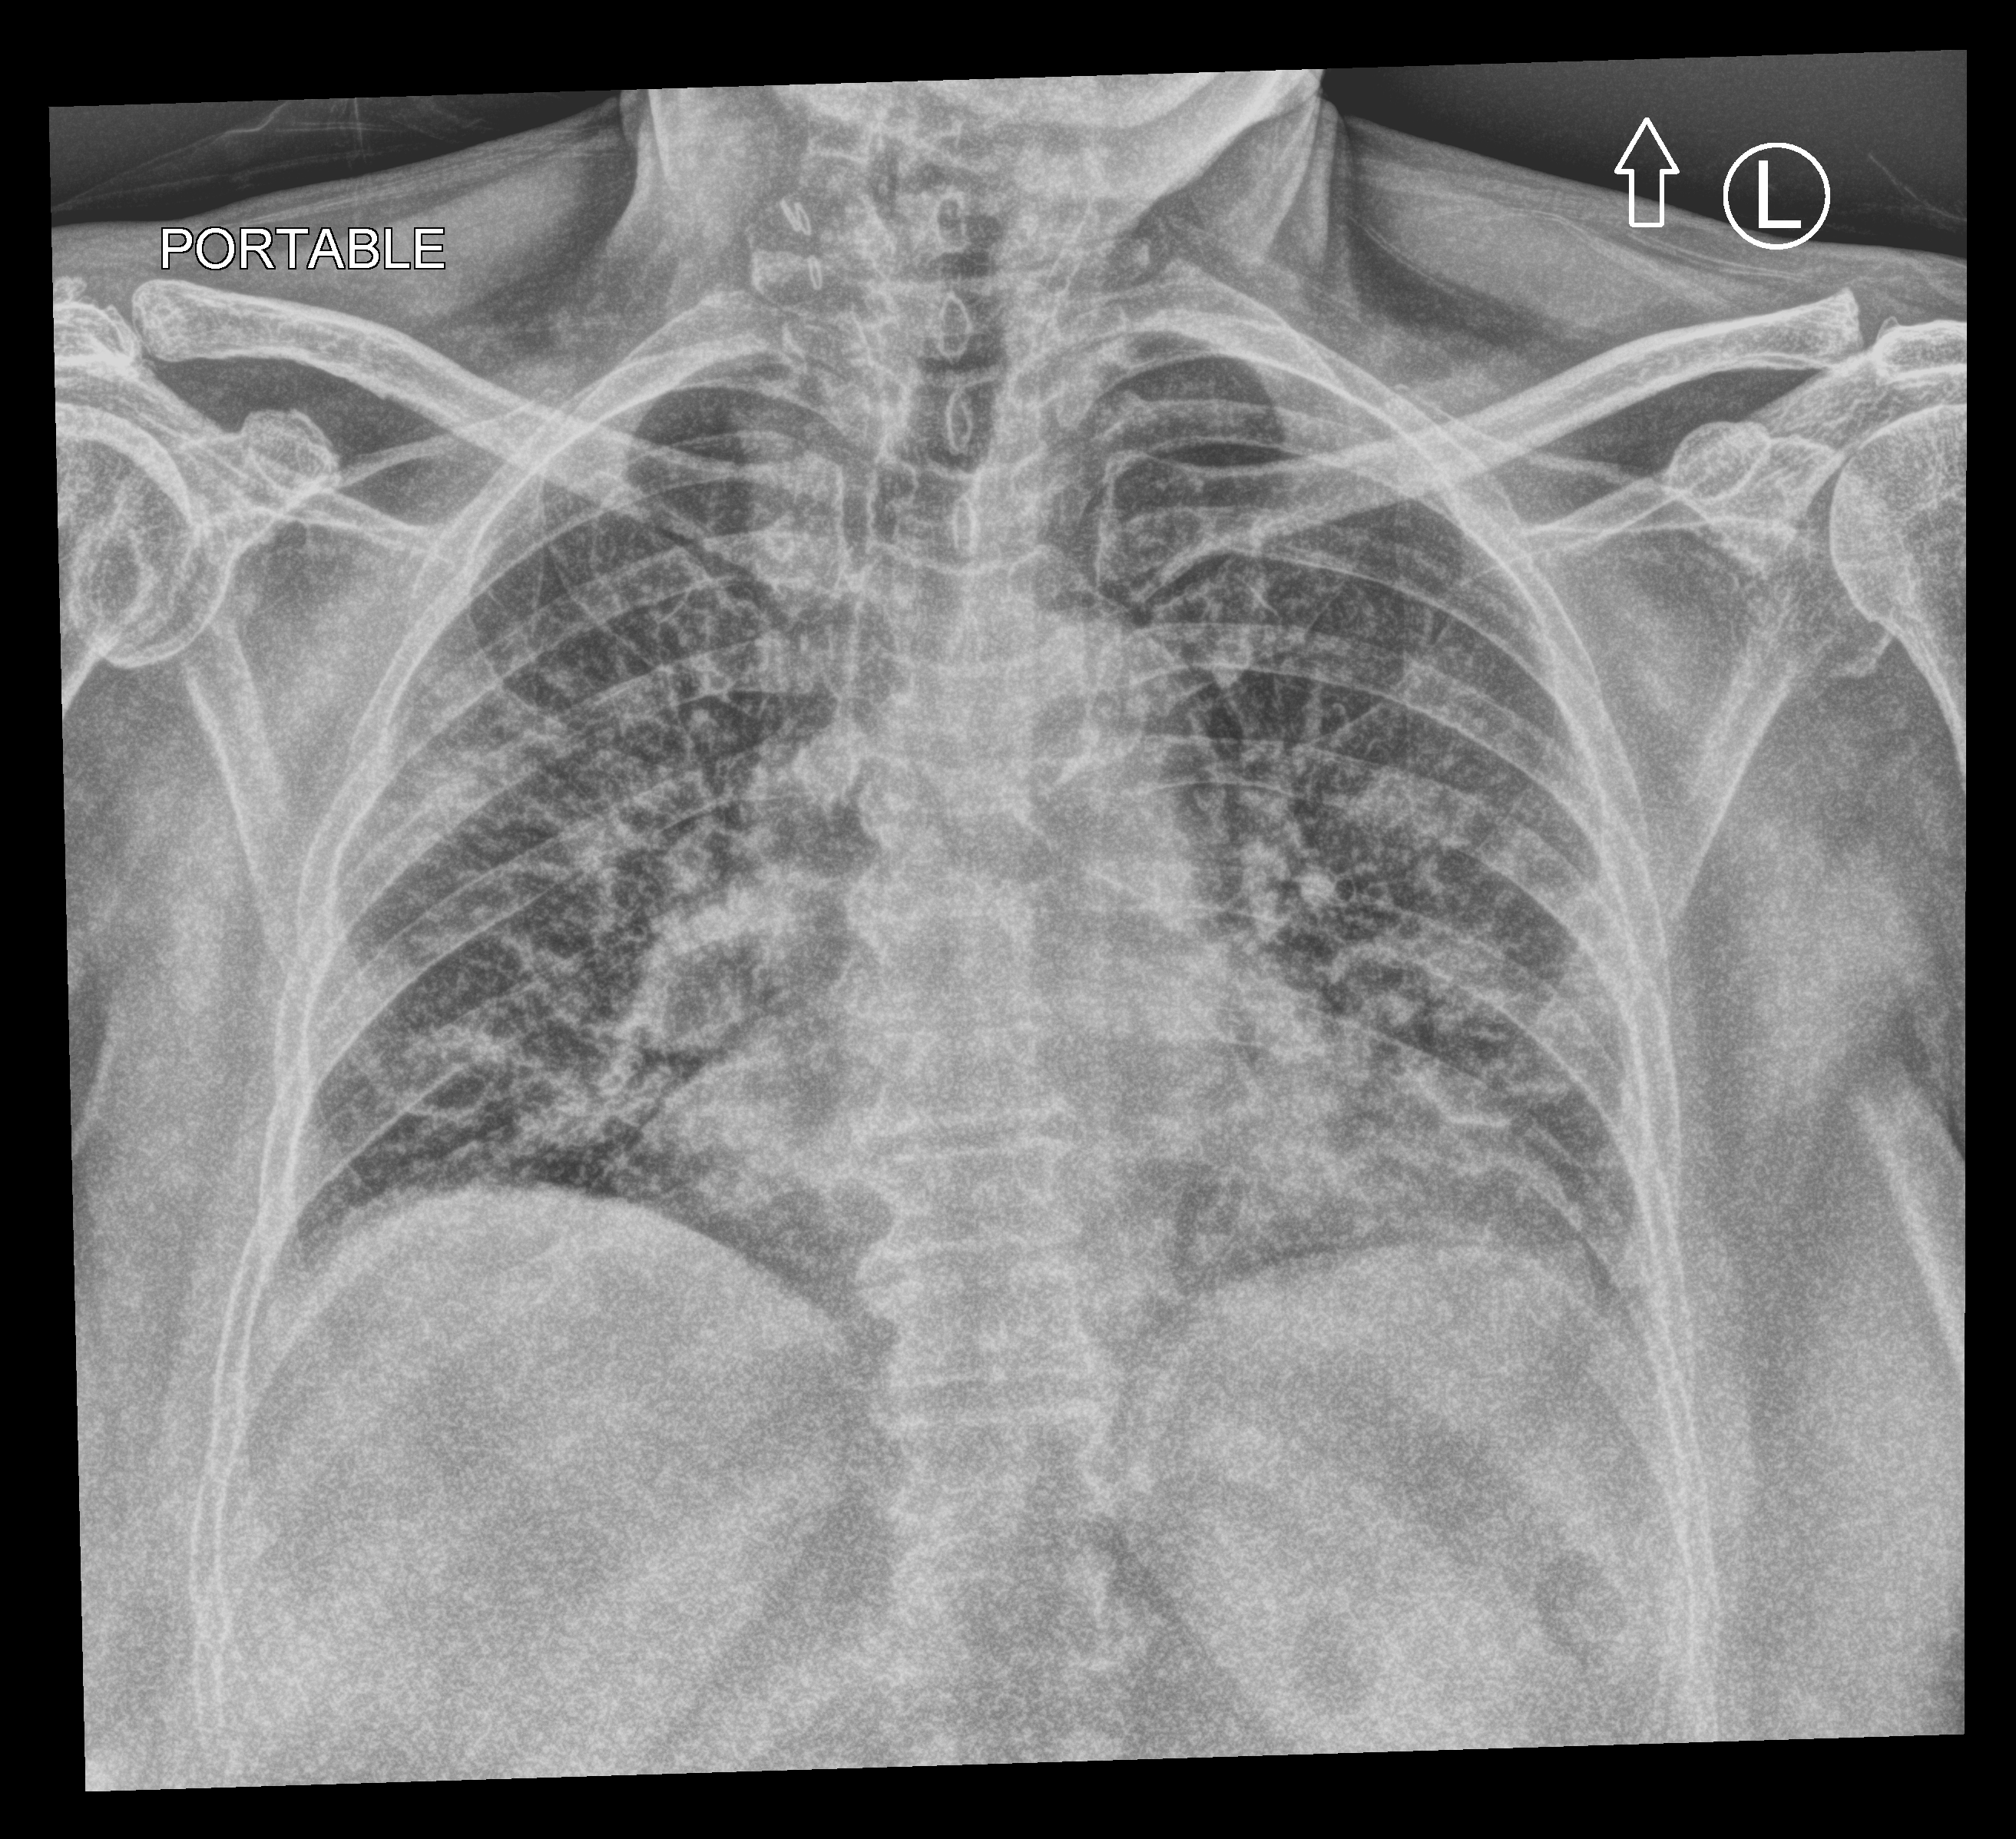
Chest X-ray (portable); anteroposterior (AP) projection. Female patient hospitalised with COVID-19, age 75–90 years.
From the hospital-stay record, not from the radiograph (when in the stay this image was taken is not recorded): smoking status (admission record): never; other chronic lung disease (admission record): no.